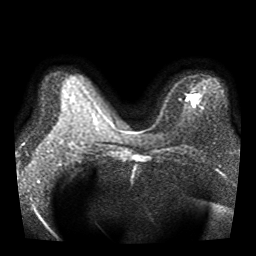
Breast MRI, one axial slice; slice 21 of 40 in the series (ordered by position); diffusion-weighted series; image 2 of 4 stored at this slice position (different b-values; order by instance number); 1.5 T; 5 mm slice thickness; 256 × 256 image matrix. Female patient.
Outlined on this slice (expert manual segmentation):
- tumour on diffusion-weighted imaging: bounding box (x1, y1, x2, y2) in pixels: (184, 94, 201, 106)